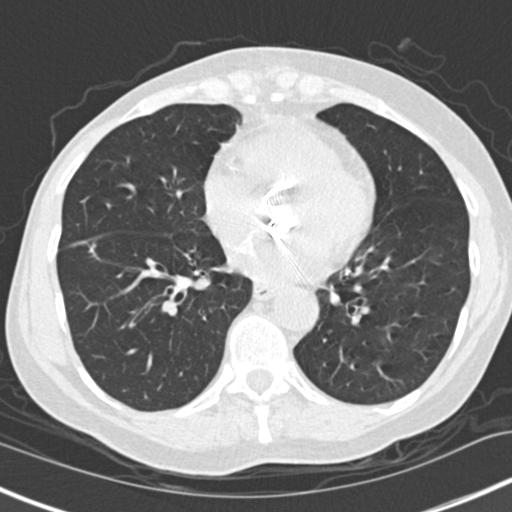
Low-dose screening chest CT, one axial slice. 120 kVp. Lung window (W 1500 / L -600 HU). 512 × 512 image matrix.
Annotated regions visible in this slice (outlined manually by an expert reader):
- lesion 1 (tumor, lower lobe of right lung): bounding box <90,245,95,255> (left, top, right, bottom; pixels)